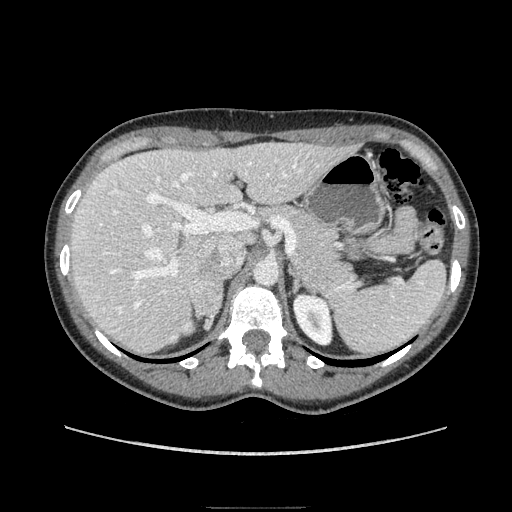
Contrast-enhanced abdominal CT, one axial slice; position 118 of 193 along the scan axis; soft-tissue window (W 400 / L 40 HU); 1.25 mm slice thickness; 512 × 512 image matrix, field of view 380 × 380 mm. Female patient. Case-level facts recorded for this patient, not image findings: diagnosis: adrenocortical carcinoma; tumour side: right adrenal; tumour size at pathology: 3 cm; Ki-67 index: 4 %; stage (as recorded): 1.
Annotated regions visible in this slice (semi-automatically segmented with operator editing):
- mass: bounding box (x1, y1, x2, y2) in pixels: (192, 279, 223, 327)